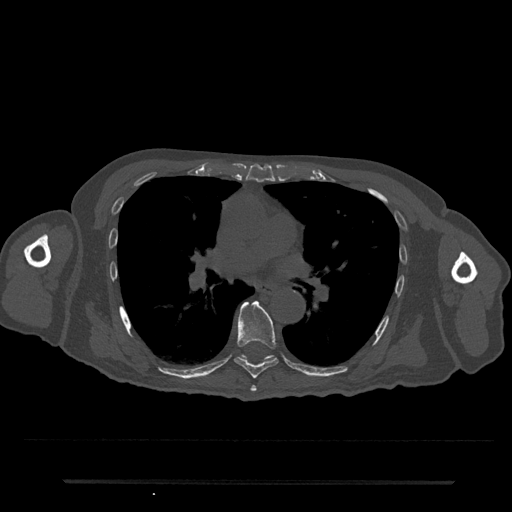
CT including the spine, one axial slice; slice 471 of 797 in the series (ordered by position); bone window (W 1800 / L 400 HU); 0.5 mm slice thickness; 512 × 512 image matrix, field of view 427 × 427 mm. Male patient, age 74 years. Case-level facts recorded for this patient, not image findings: primary cancer: prostate.
Outlined on this slice (semi-automatic segmentation, software-assisted and operator-edited):
- T6 vertebra: bounding box [x1, y1, x2, y2] px = [250, 385, 256, 392]
- T7 vertebra: [234, 301, 279, 379]
- T8 vertebra: [240, 354, 274, 362]